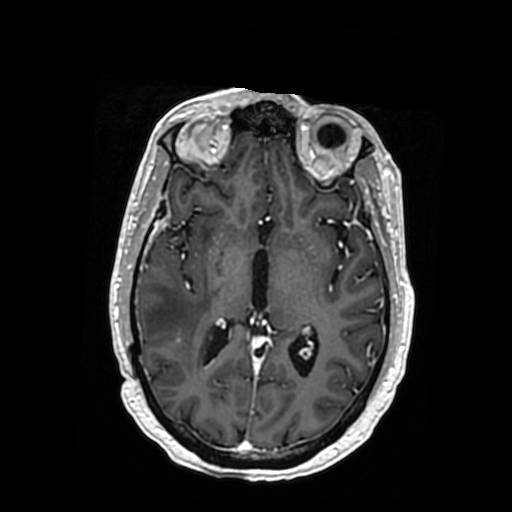
Brain MRI from a brain-tumour surgery series, one axial slice; position 188 of 364 along the scan axis; T1-weighted post-contrast; 512 × 512 image matrix, field of view 260 × 260 mm. Case-level facts recorded for this patient, not image findings: histopathology: Oligodendroglioma; WHO grade: 3; IDH mutation: yes; tumour location: Right Posterior Temporal Inferior Parietal.
Outlined on this slice (manually delineated by an expert):
- tumour: box from (x=196, y=337) to (x=200, y=338) px